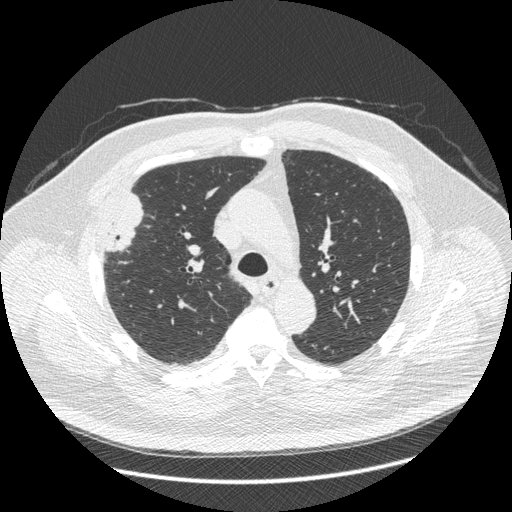
Low-dose screening chest CT, one axial slice. Slice 297 of 426 in the series (ordered by position). Lung window (W 1500 / L -600 HU). 1.25 mm slice thickness. 512 × 512 image matrix.
Structures marked on this image (outlined manually by an expert reader):
- lesion 1 (tumor, upper lobe of right lung): bounding box (x1, y1, x2, y2) in pixels: (105, 193, 143, 252)